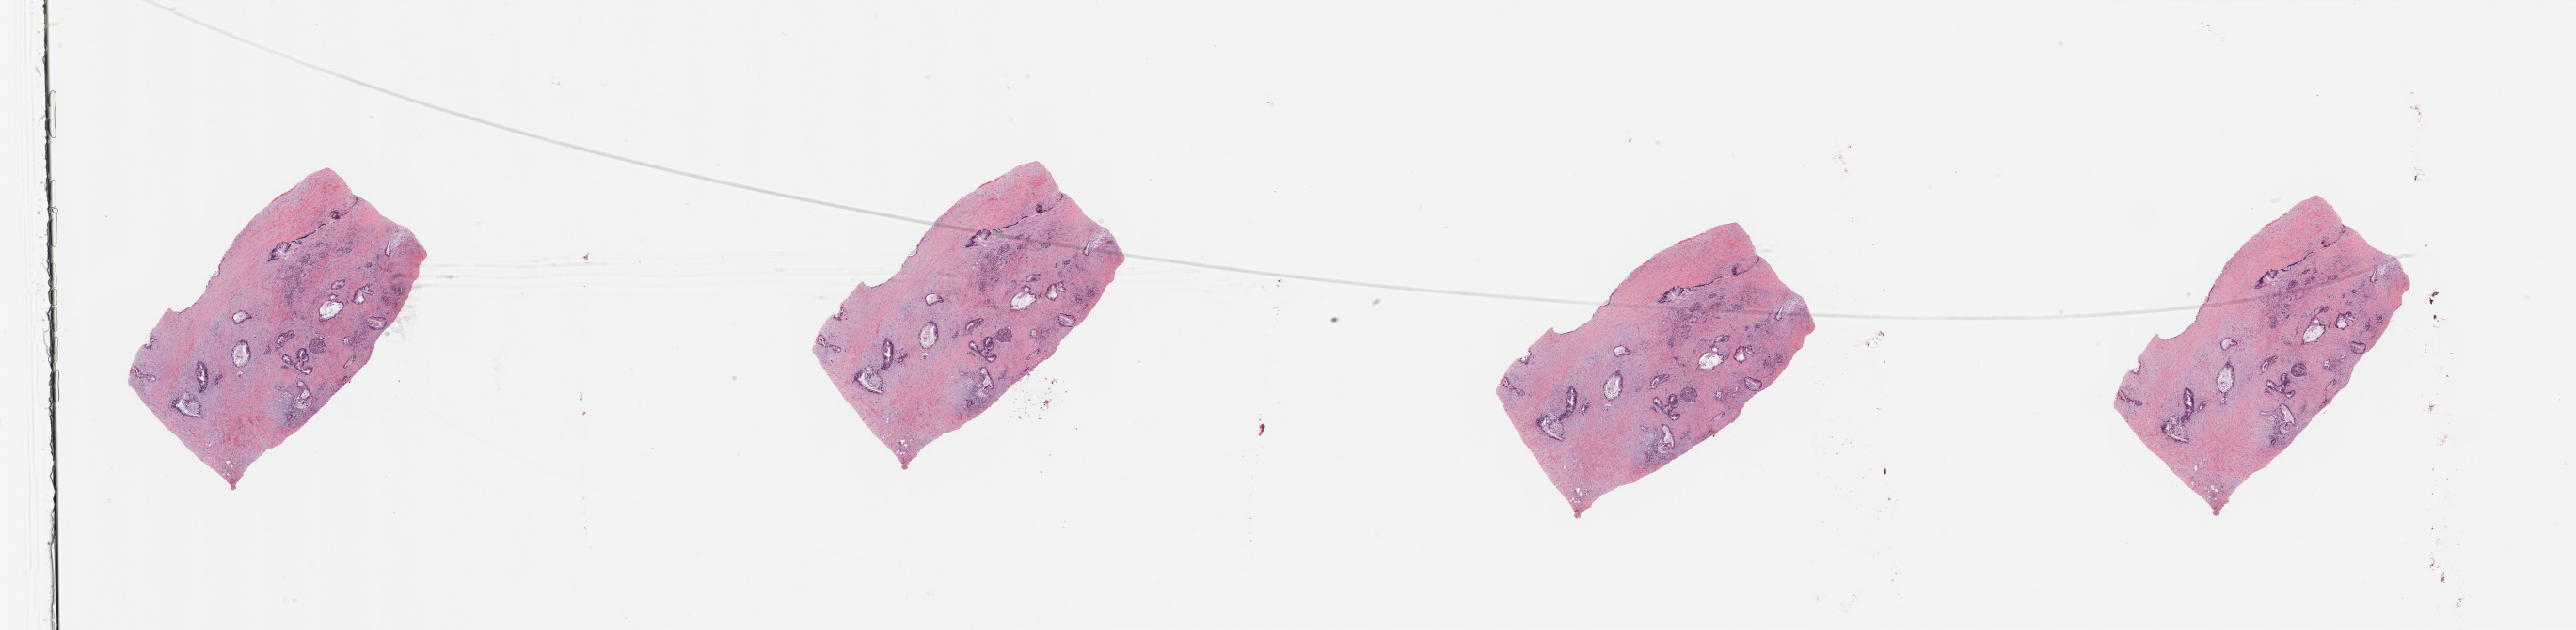
Digitized H&E-stained tissue section (whole slide), shown as a low-resolution overview of the whole scanned area (about 43.3 x 10.6 mm, from a 20x scan), tumour tissue sample, sampled site: pancreas. 62-year-old male patient. Histologic grade: G3 (poorly differentiated). Composition of this section per pathologist review: tumour nuclei 25%, necrosis 0%.
- diagnosis: Infiltrating duct carcinoma, NOS
- AJCC pathologic stage: IIA